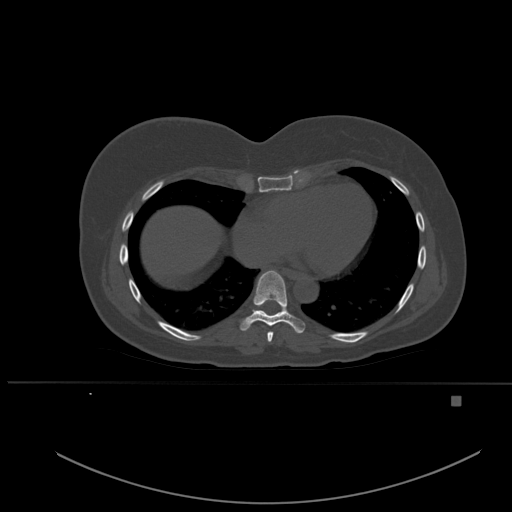
CT including the spine, one axial slice; bone window (W 1800 / L 400 HU); 512 × 512 image matrix, field of view 443 × 443 mm. Patient: female, 49 years. Case-level facts recorded for this patient, not image findings: primary cancer: breast; vertebrae with lytic lesions (as recorded): L3, T12, L4.
Outlined on this slice (semi-automatic segmentation, software-assisted and operator-edited):
- T7 vertebra: bounding box <267,331,273,342> (left, top, right, bottom; pixels)
- T8 vertebra: <240,270,305,333>
- T9 vertebra: <253,309,258,311>